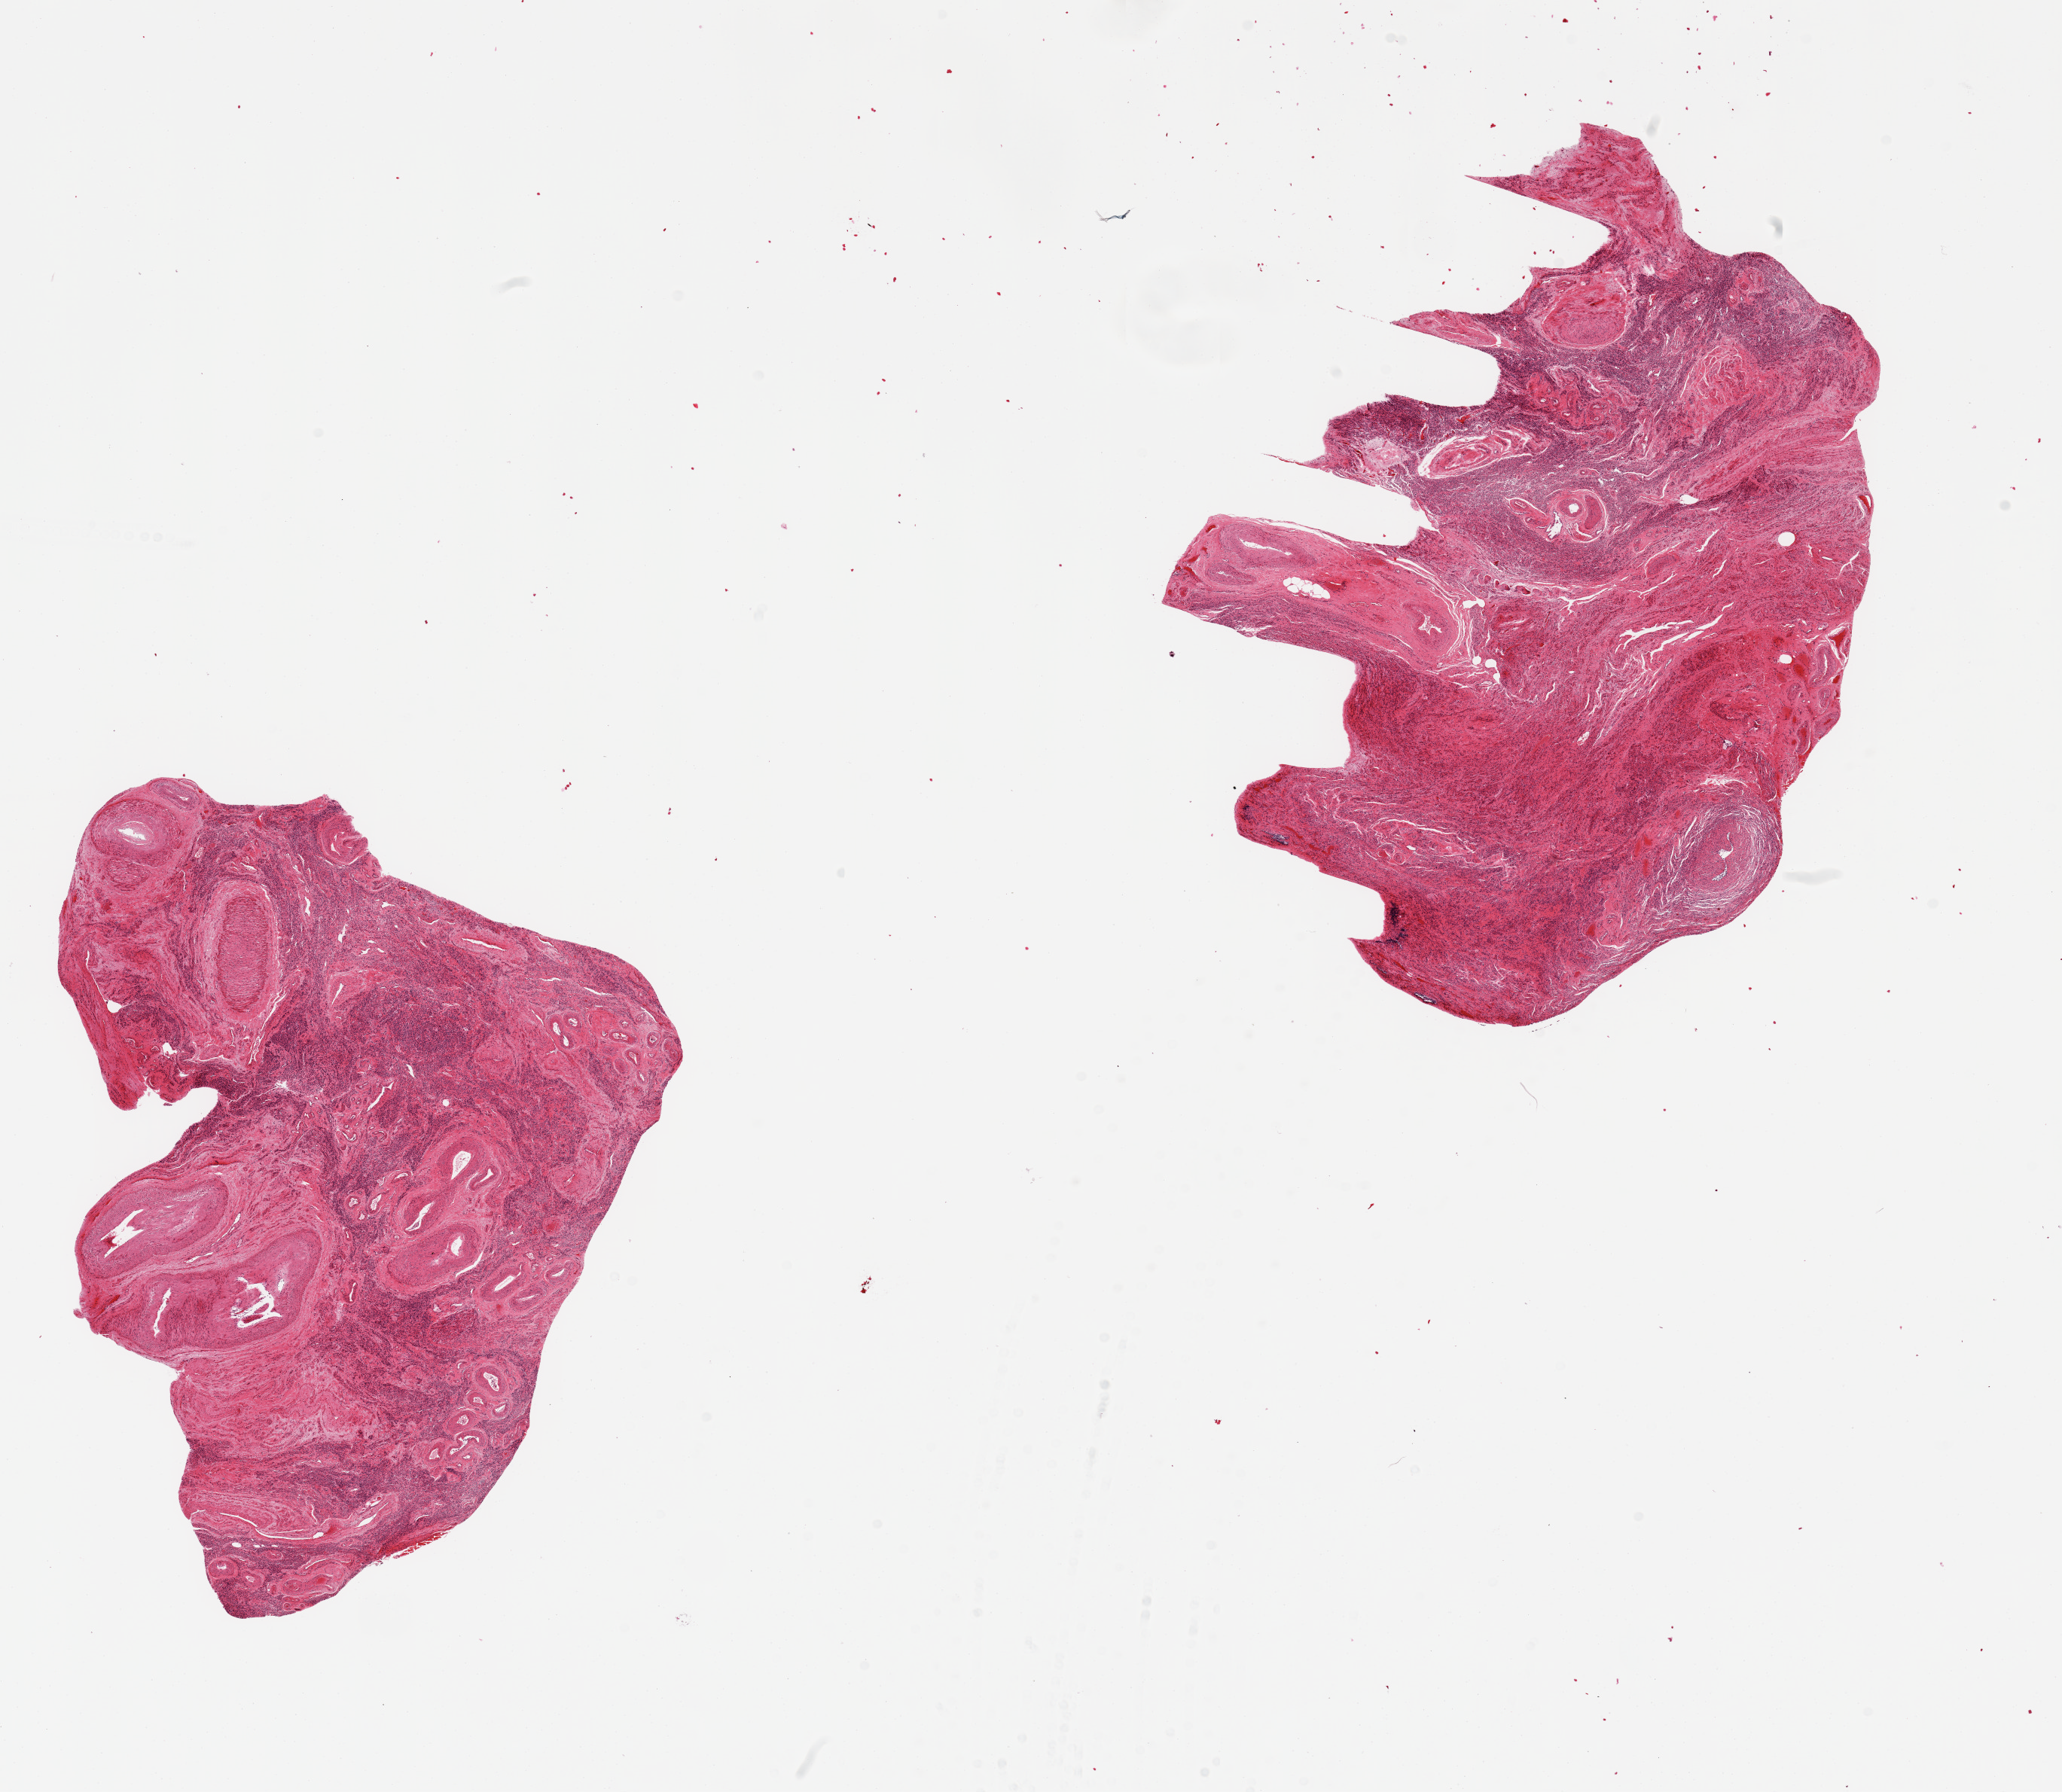
Whole-slide image, haematoxylin and eosin stain, low-resolution overview of the scanned area, about 21.7 x 18.8 mm (acquisition: 20x scan); PAXgene-fixed, paraffin-embedded tissue; target tissue: uterus; donor tissue sample. Donor: female.
Pathologist's review note for this sample: 2 pieces; largely myometrium, no glands.